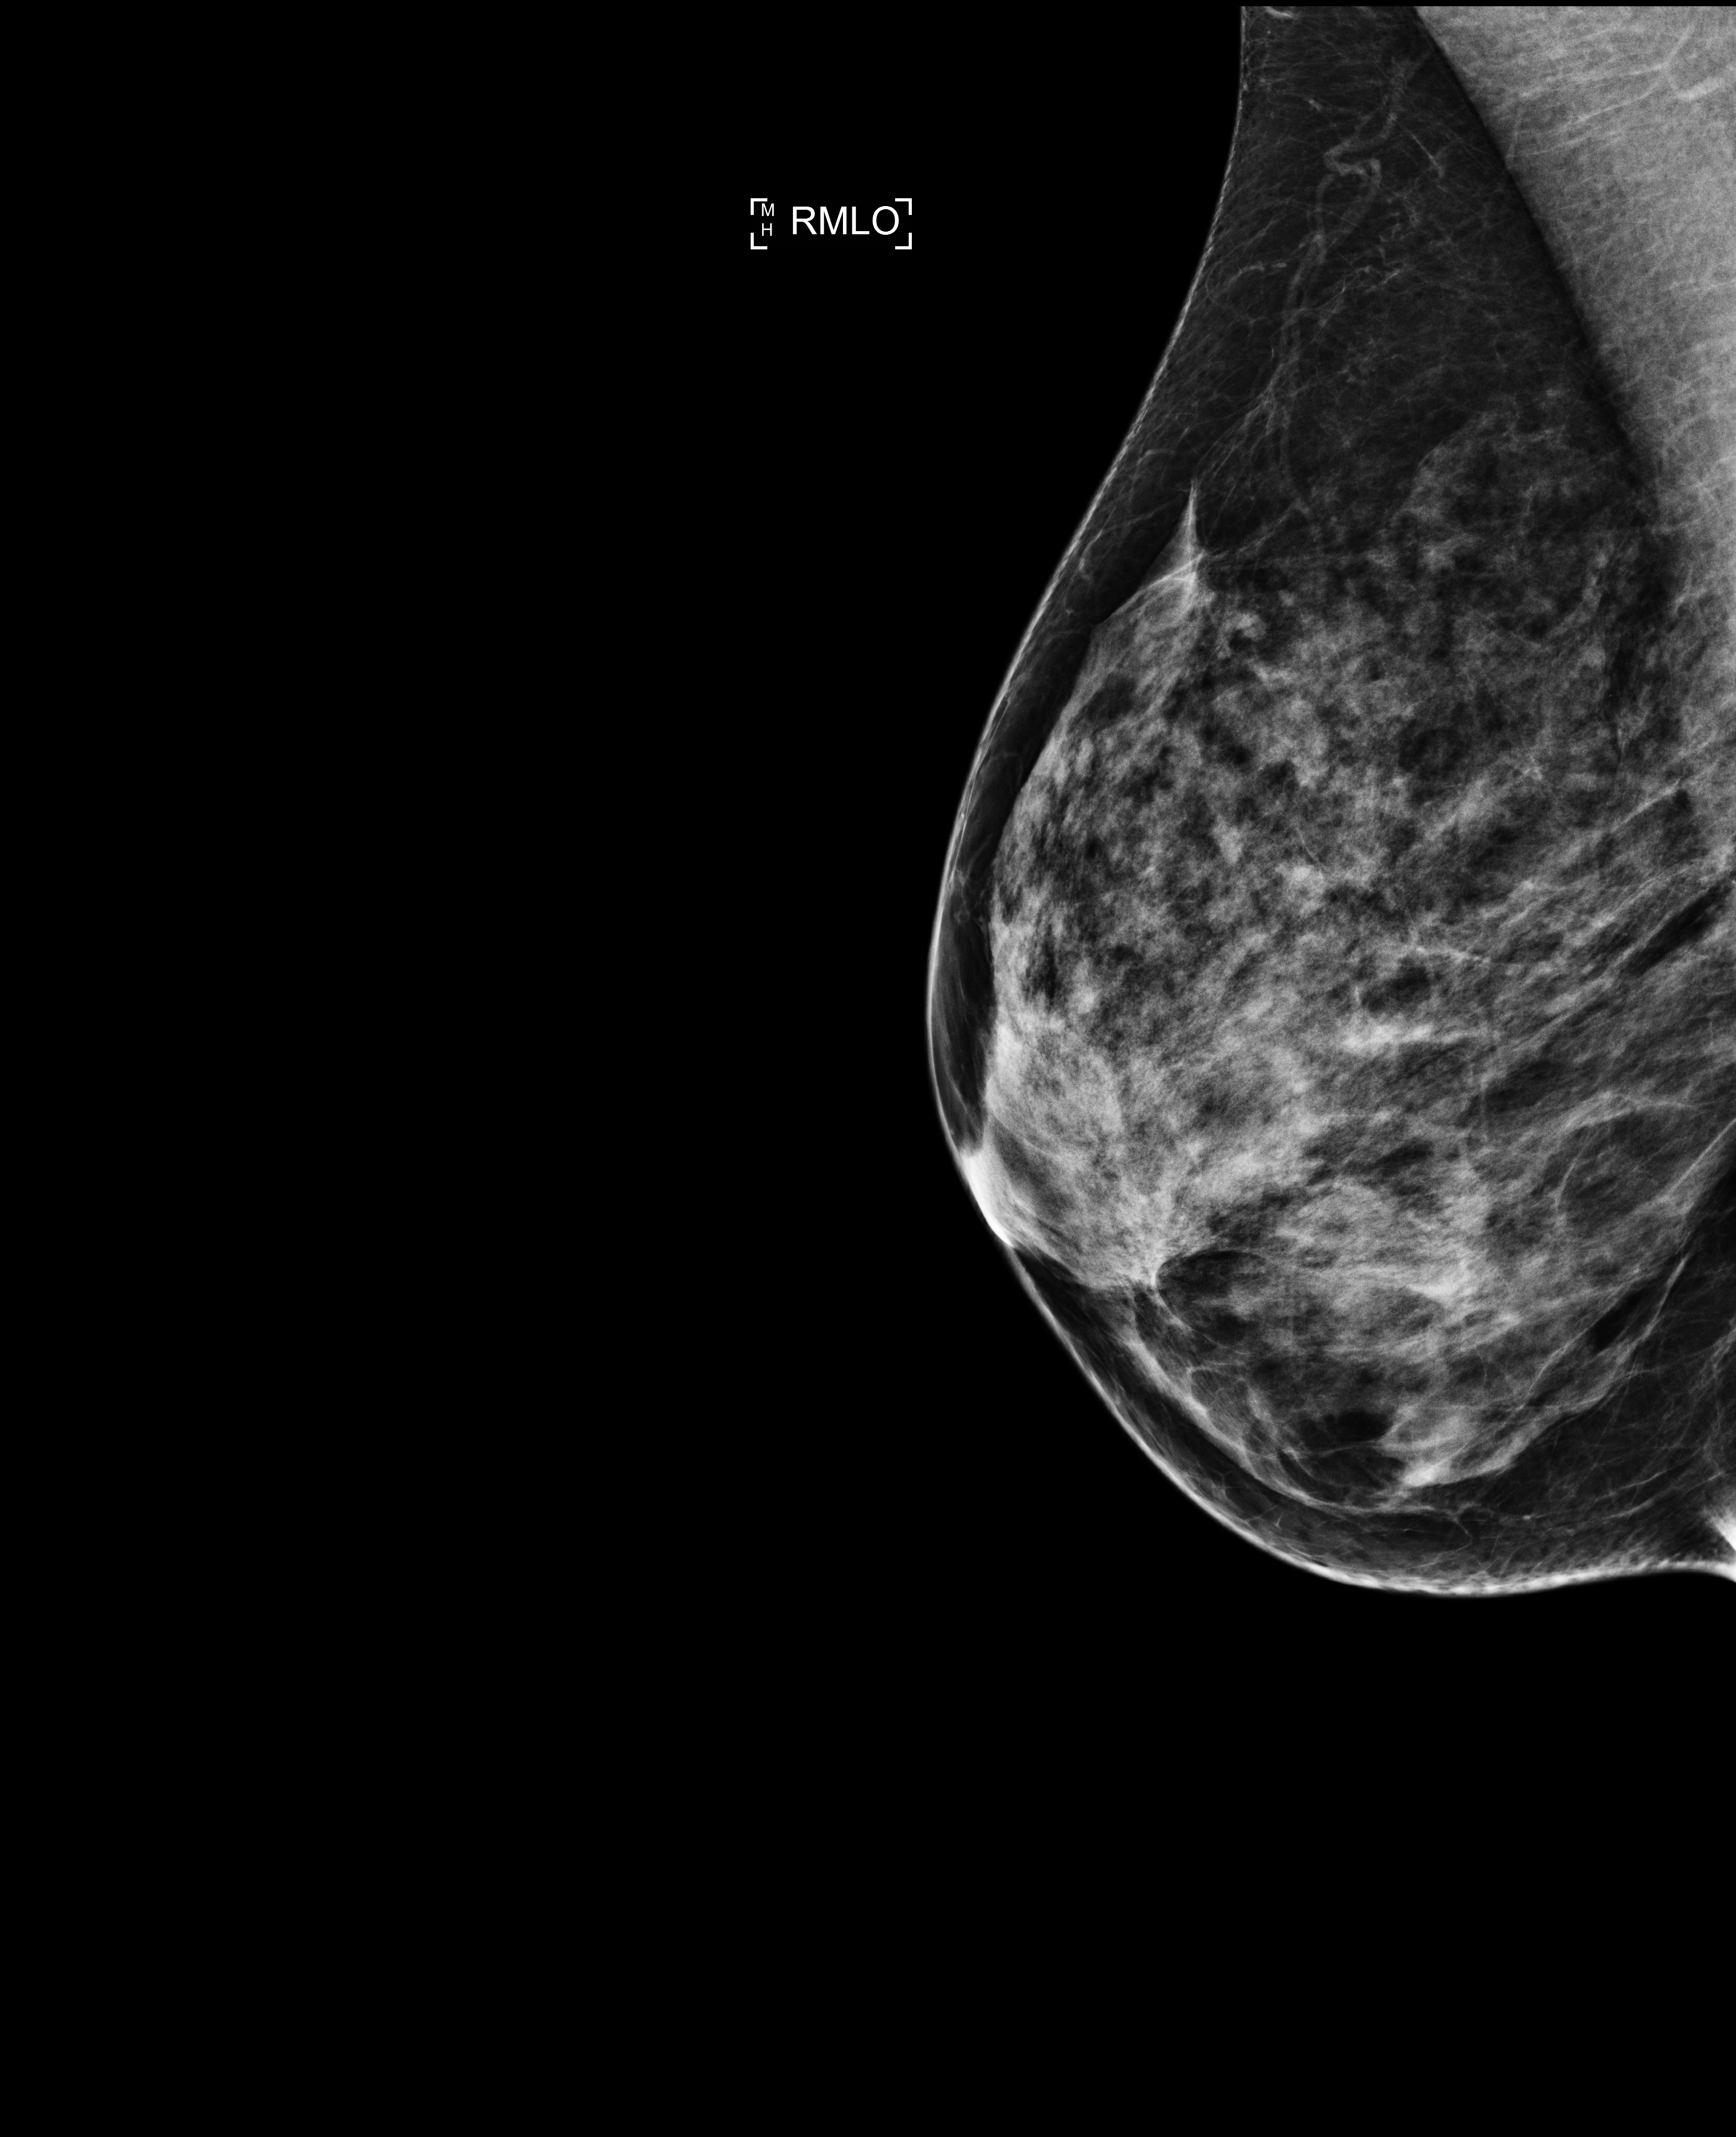
Full-field digital mammogram (FFDM), right breast, mediolateral oblique (MLO) view, annual screening mammography examination, compressed breast thickness 54 mm, system: Selenia Dimensions. Patient: female, 41 years.
- BI-RADS breast density category at the screening exam (both breasts, scale 1–4): 4
- final BI-RADS assessment for this screening round (tomosynthesis exam, both breasts): category 1
- recall: no recall after this screen